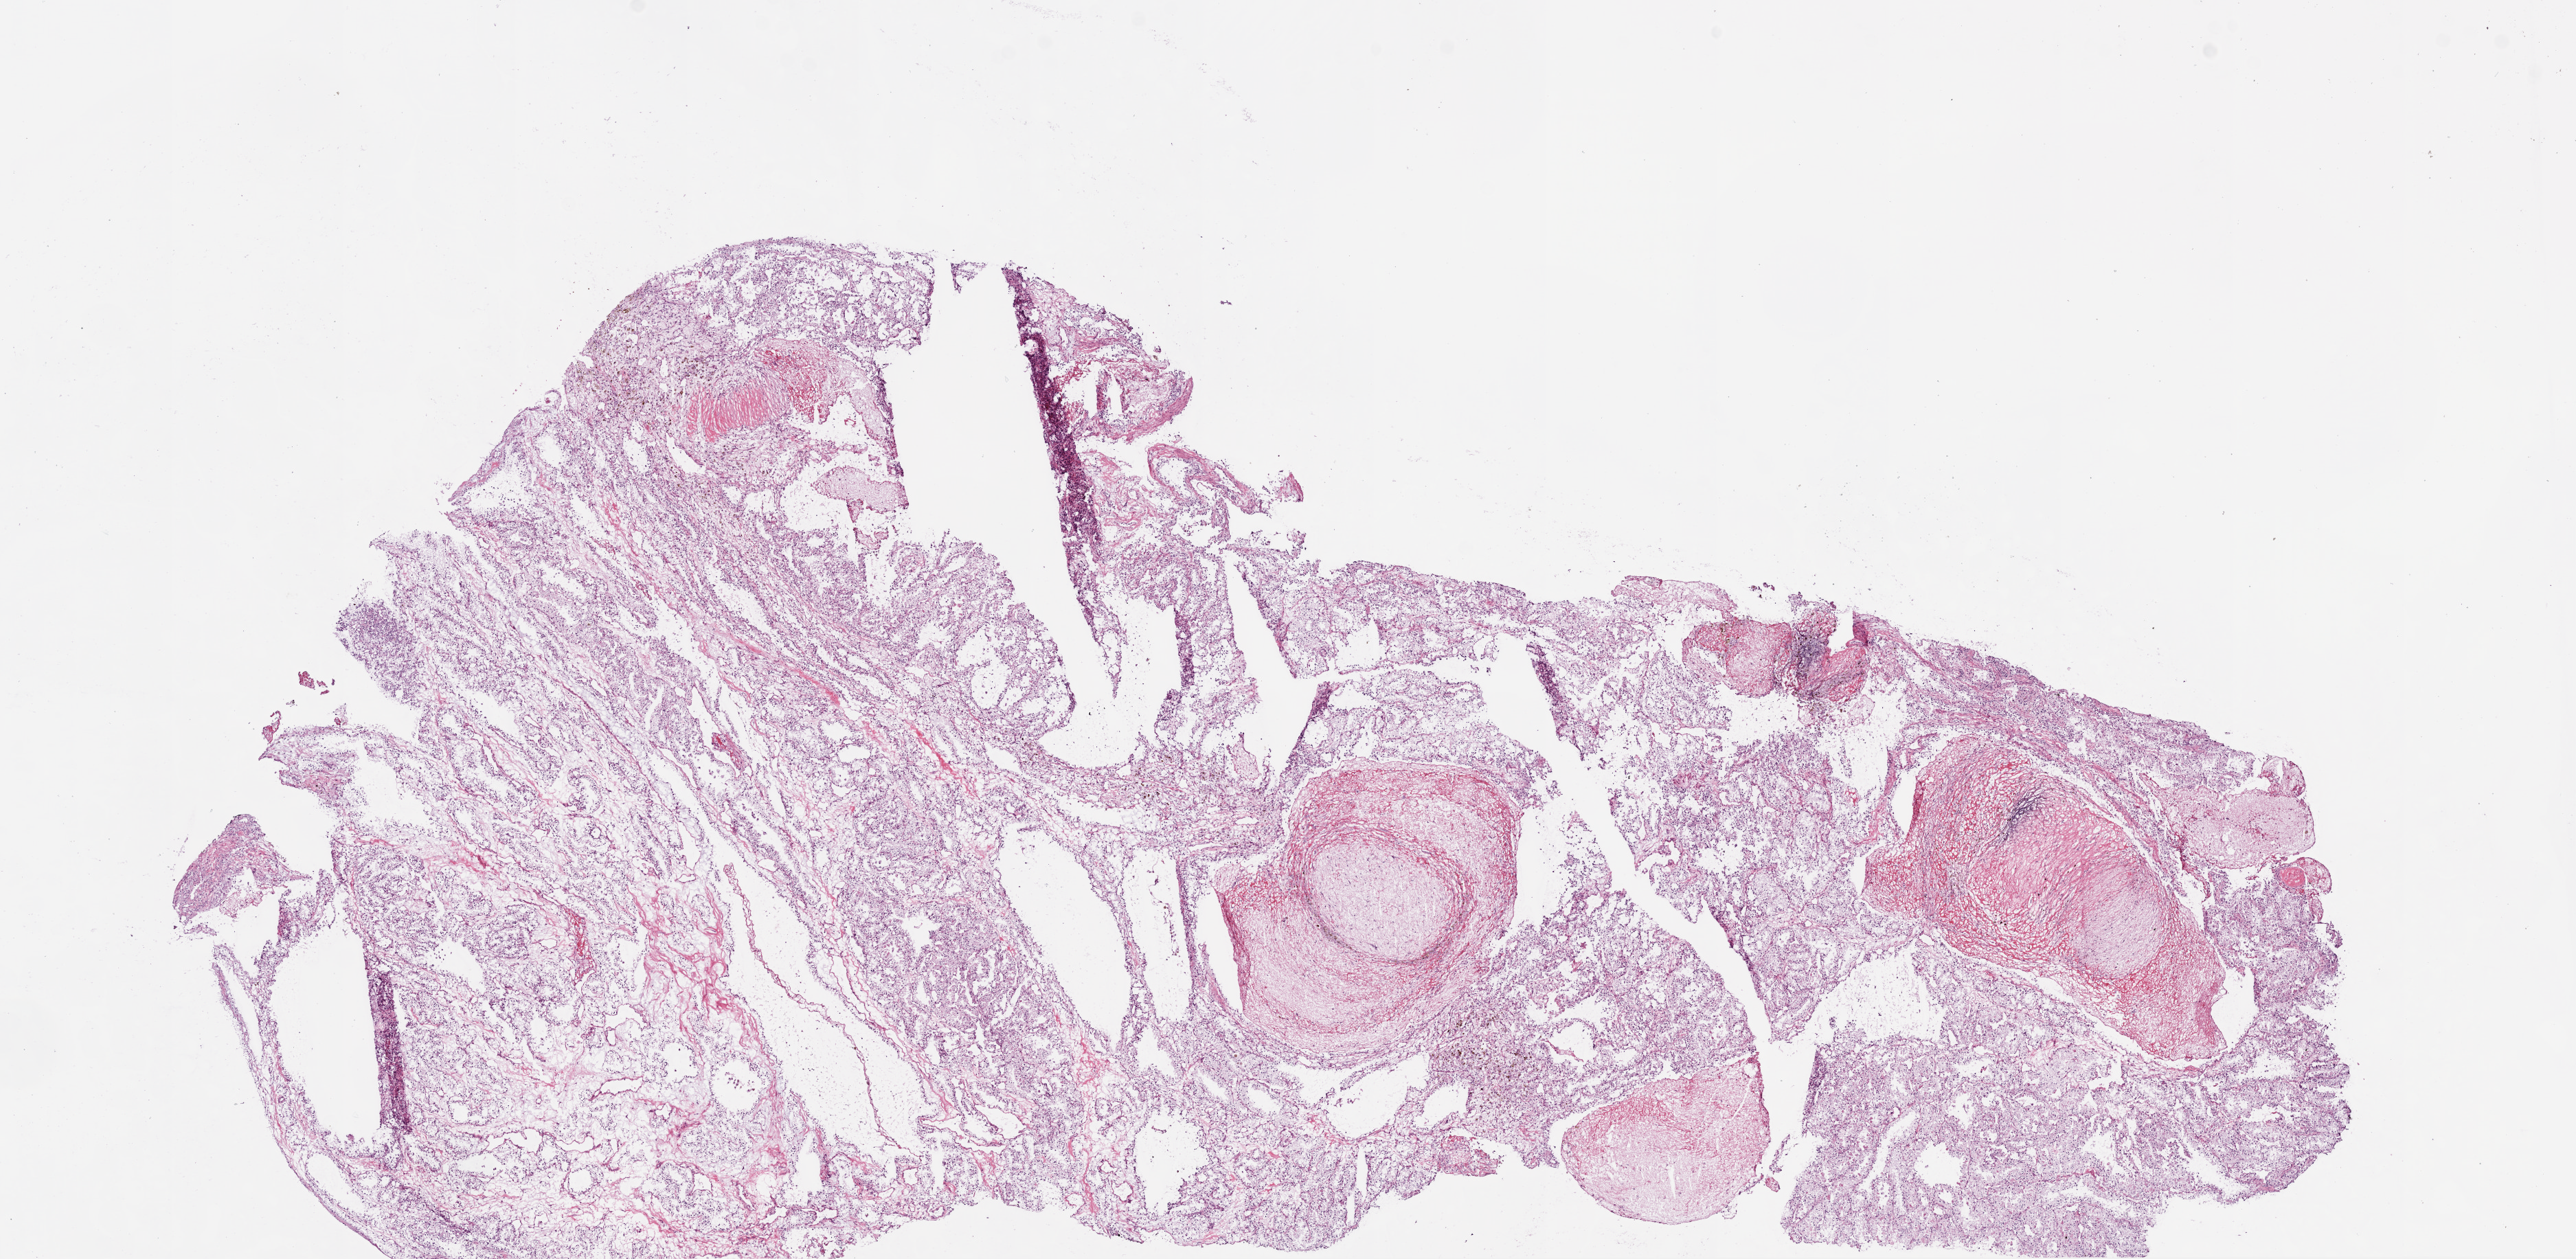
Digitized Hematoxylin and eosin (H&E) stained tissue section (whole slide) — low-resolution overview of the scanned area, about 15.0 x 7.4 mm (acquisition: 20x scan), frozen section from the bottom of the tissue portion, primary tumour sample from the kidney. Patient: male, age at initial diagnosis 42 years. Composition of this section per pathologist review: tumour cells 80%, tumour nuclei 90%.
Histologic diagnosis: Clear cell adenocarcinoma, NOS.